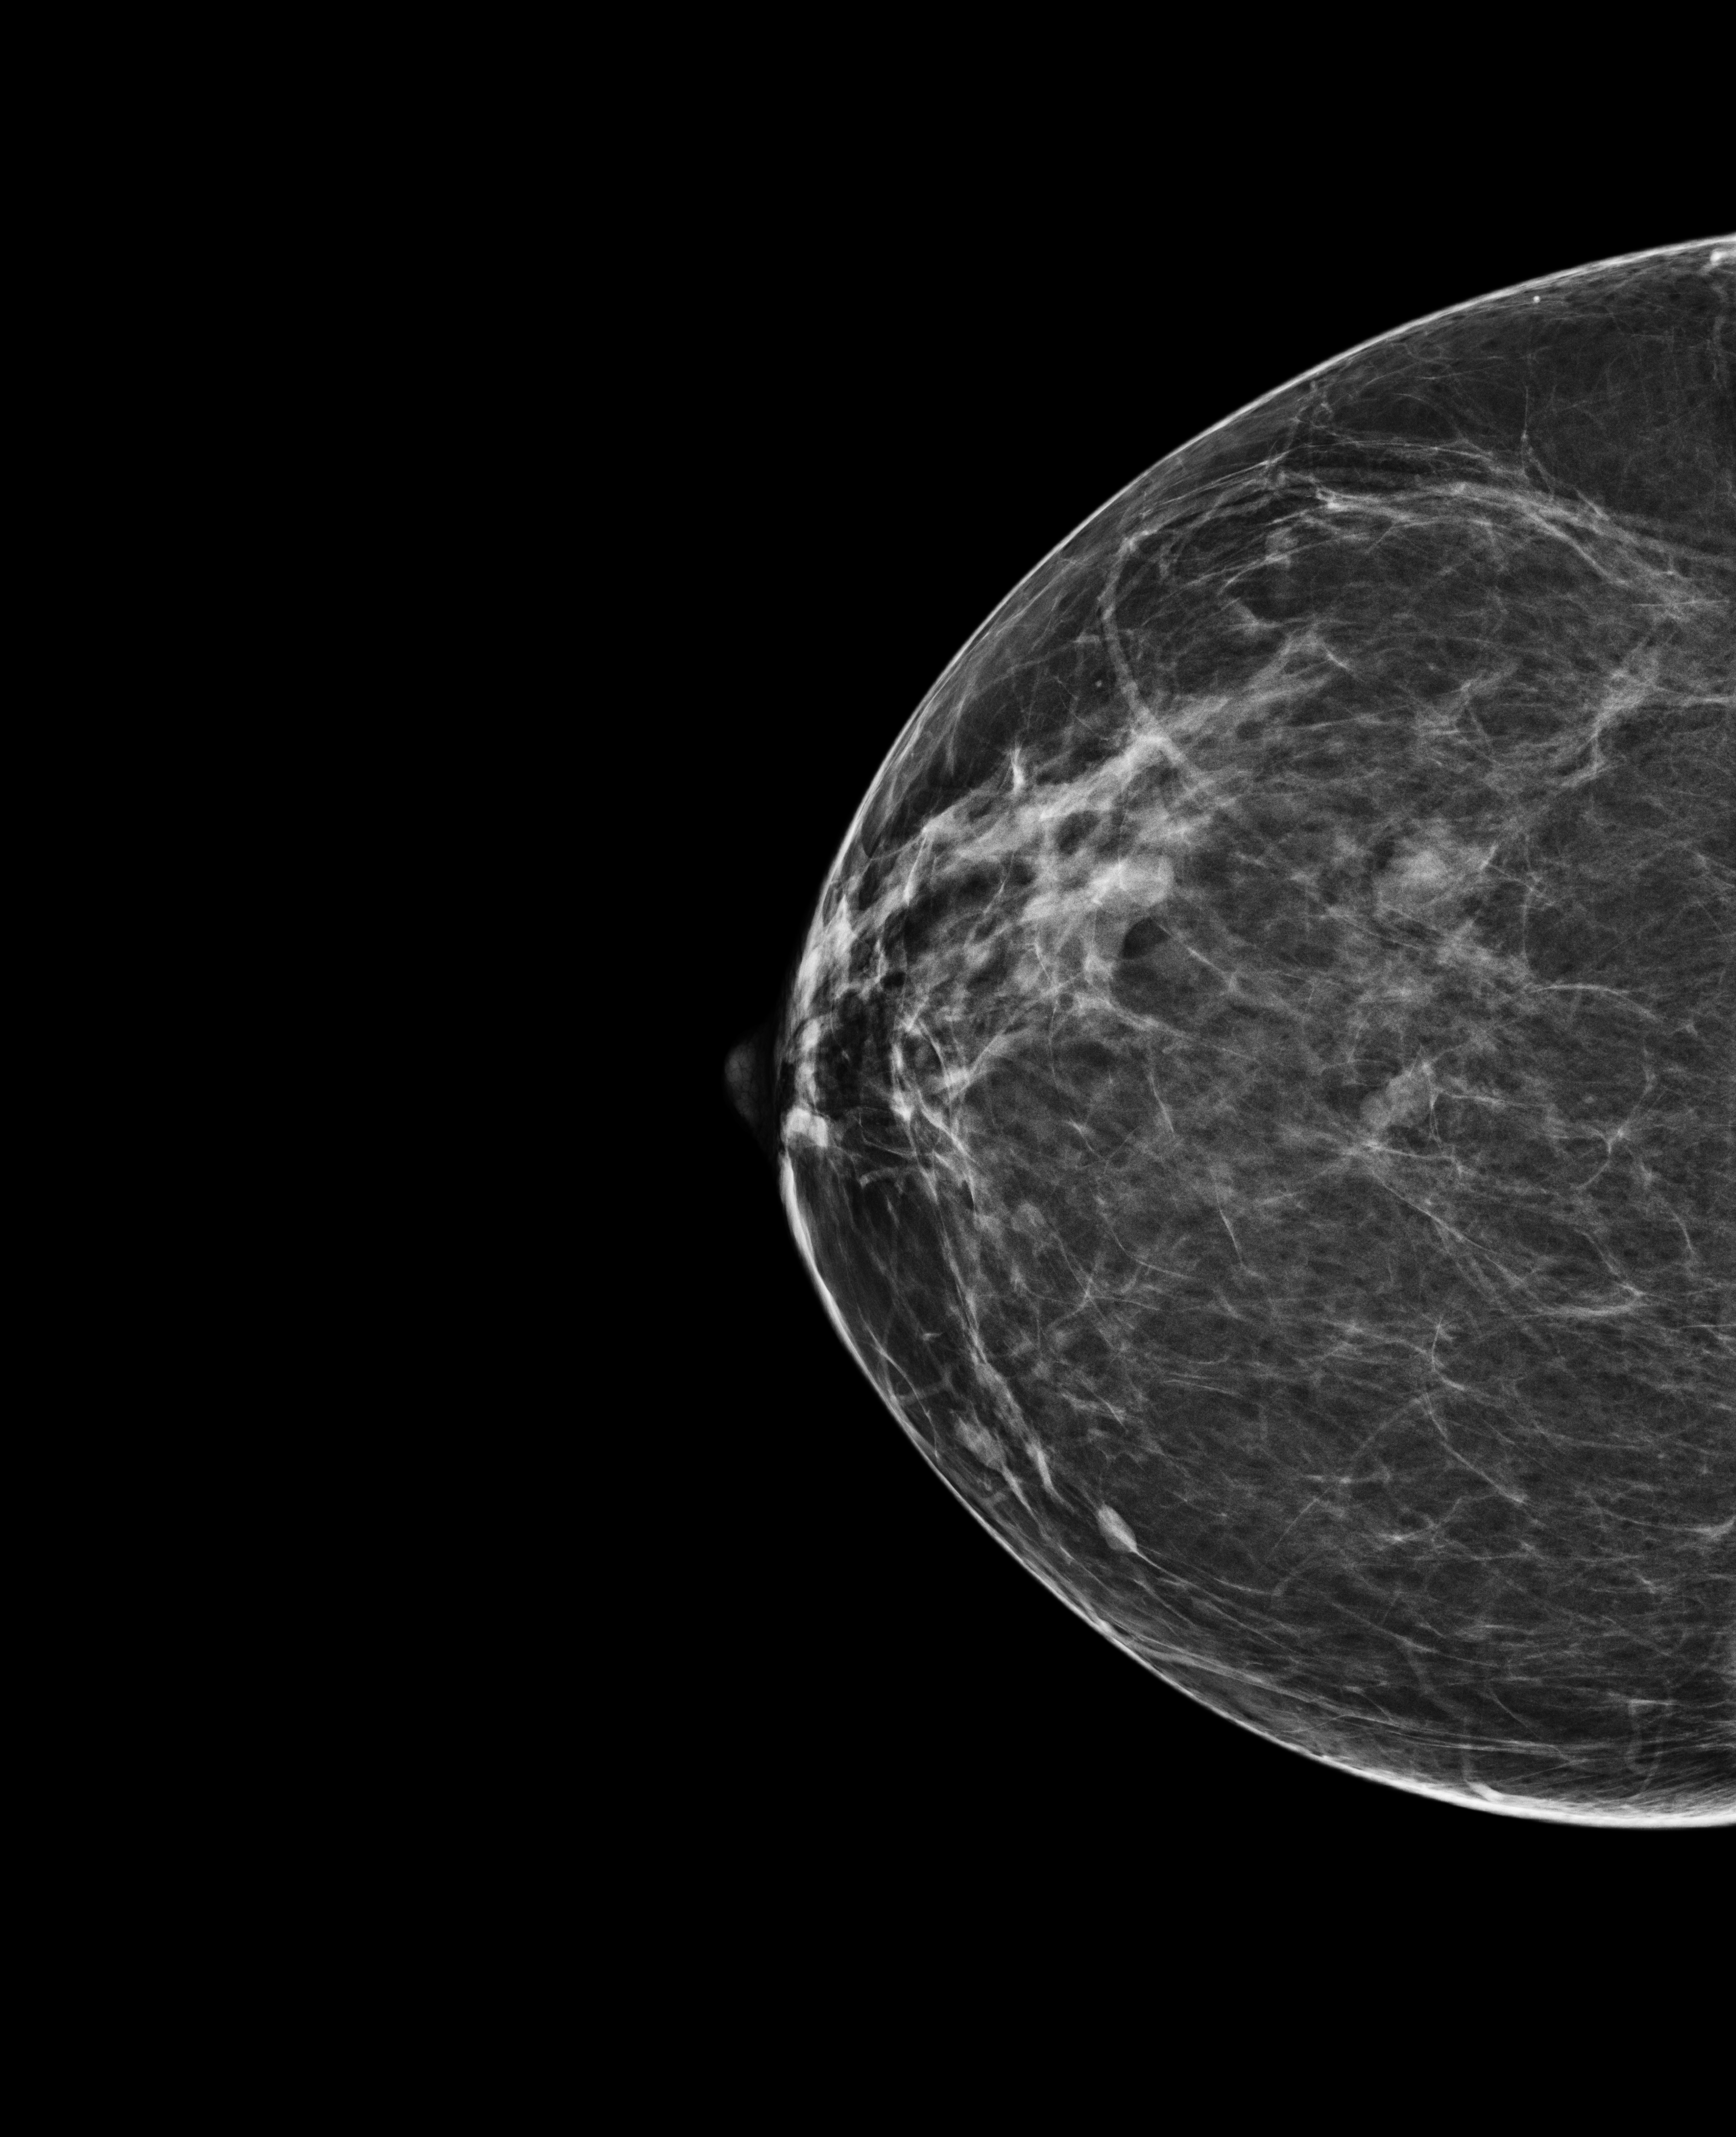
Annual screening mammography examination. Patient aged 65 years (female).
Image type: full-field digital mammogram. Breast: right. Projection: cranio-caudal projection.